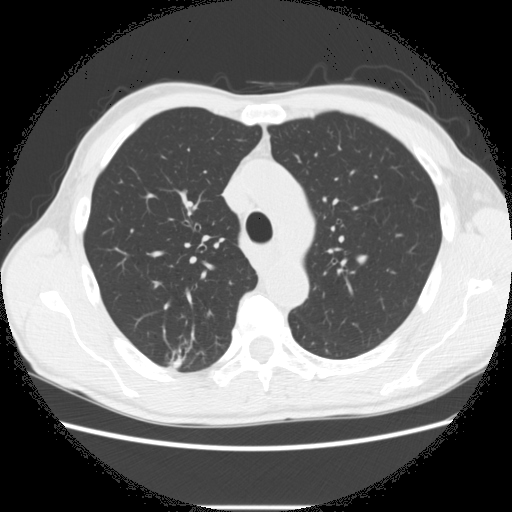
Low-dose screening chest CT, one axial slice. Position 202 of 282 along the scan axis. Reconstruction kernel STANDARD. Lung window (W 1500 / L -600 HU). 2.5 mm slice thickness. 512 × 512 image matrix, field of view 360 × 360 mm.
Outlined on this slice (expert manual segmentation):
- lesion 1 (tumor, upper lobe of right lung): bounding box (x1, y1, x2, y2) in pixels: (169, 356, 184, 370)